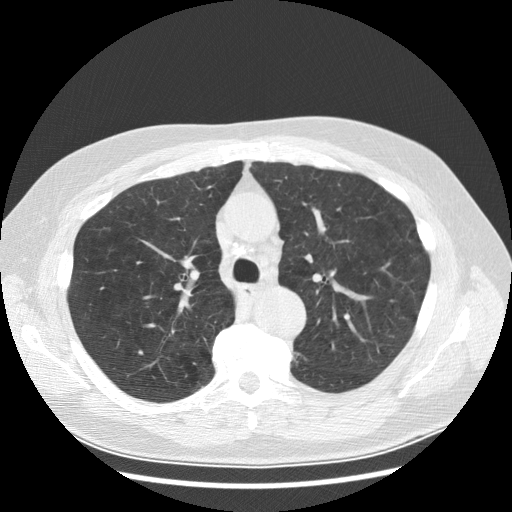
Low-dose screening chest CT, one axial slice; reconstruction kernel STANDARD; 120 kVp; lung window (W 1500 / L -600 HU); 2.5 mm slice thickness; 512 × 512 image matrix, field of view 370 × 370 mm.
Outlined on this slice (outlined manually by an expert reader):
- lesion 1 (tumor, lower lobe of left lung): bounding box <293,352,307,365> (left, top, right, bottom; pixels)